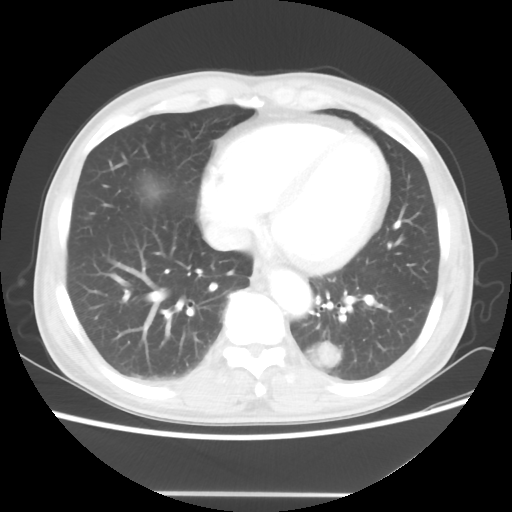
Chest CT, one axial slice. Slice 19 of 60 in the series (ordered by position). Lung window (W 1500 / L -600 HU). 5 mm slice thickness. 512 × 512 image matrix, field of view 360 × 360 mm. Patient: male, 55 years. Case-level facts recorded for this patient, not image findings: clinical TNM (as recorded): T1c N3 M0; histopathological grade: G3.
Annotated regions visible in this slice (bounding box drawn by a radiologist):
- lung tumour (recorded histology: small cell carcinoma): bounding box [x1, y1, x2, y2] px = [307, 335, 342, 369]